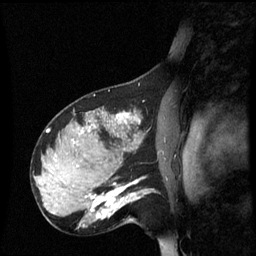
Breast MRI (dynamic contrast-enhanced), one sagittal slice. Slice 40 of 60 in the series (ordered by position). Dynamic contrast-enhanced series, image 2 of 3 at this slice position (ordered by acquisition). 1.5 T. TE 4.2 ms, TR 8.9 ms. 2.2 mm slice thickness. 256 × 256 image matrix, field of view 220 × 220 mm. Patient: female, 31 years. Case-level facts recorded for this patient, not image findings: setting: breast cancer imaged before/during neoadjuvant chemotherapy; receptor status: HR-positive, HER2-negative.
Outlined on this slice (semi-automatic segmentation, software-assisted and operator-edited):
- analysis volume of interest (the breast-tissue region the enhancement analysis was run in; not a lesion): bounding box (x1, y1, x2, y2) in pixels: (90, 180, 149, 225)
- tumour enhancement mask (voxels above the 70 % enhancement threshold inside the analysis volume of interest): (91, 180, 139, 219)